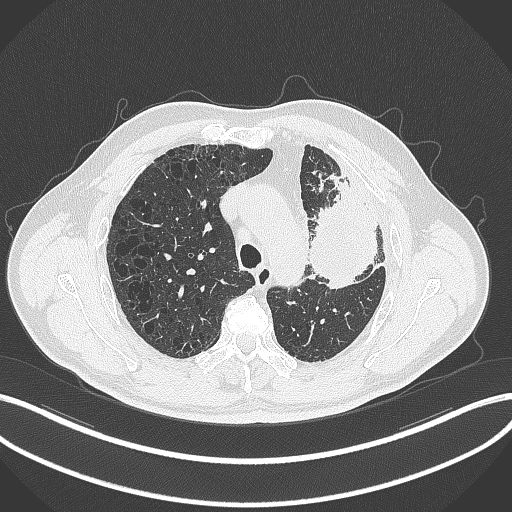
Chest CT, one axial slice. Position 230 of 297 along the scan axis. 120 kVp. Lung window (W 1500 / L -600 HU). 512 × 512 image matrix, field of view 400 × 400 mm. Patient: male, 68 years. Case-level facts recorded for this patient, not image findings: clinical TNM (as recorded): T3 N3 M1.
Structures marked on this image (rectangle marked by the reading radiologist):
- lung tumour (recorded histology: adenocarcinoma): box from (x=300, y=167) to (x=388, y=296) px